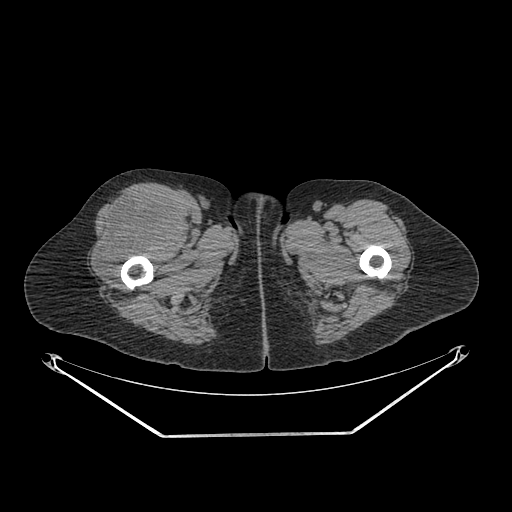
CT of an extremity soft-tissue mass (from a PET/CT study), one axial slice. Position 272 of 311 along the scan axis. Reconstruction kernel SOFT. 140 kVp. Soft-tissue window (W 400 / L 40 HU). 512 × 512 image matrix, field of view 500 × 500 mm. Female patient. Case-level facts recorded for this patient, not image findings: histological type: pleiomorphic undifferentiated sarcoma; grade: high; site of the primary tumour: right quadricep.
Structures marked on this image (expert contour drawn on MRI and transferred to this co-registered scan by the dataset authors):
- tumour plus oedema (research contour): bounding box (x1, y1, x2, y2) in pixels: (96, 192, 177, 273)
- tumour (research contour): (96, 192, 177, 273)